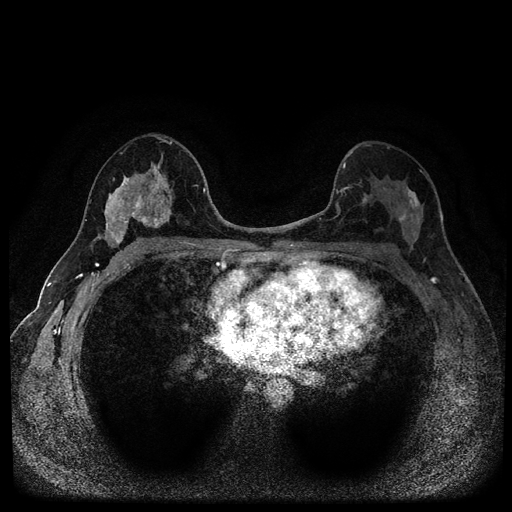
Breast MRI (dynamic contrast-enhanced, multi-phase), one axial slice; position 57 of 116 along the scan axis; dynamic contrast-enhanced series, time point 2 of 5 at this slice position (early post-contrast); 1.5 T; TE 2.7 ms, TR 5.4 ms; 2 mm slice thickness; 512 × 512 image matrix, field of view 320 × 320 mm. Female patient, age 49 years.
Annotated regions visible in this slice (semi-automatically segmented with operator editing):
- breast lesion (labelled benign in the annotation): box from (x=104, y=160) to (x=174, y=247) px